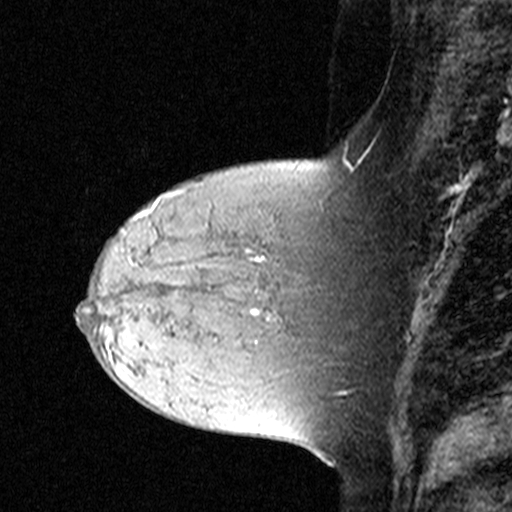
Breast MRI (dynamic contrast-enhanced), one sagittal slice. Dynamic contrast-enhanced study with each time point stored as its own series, time point 2 of 3 at this slice position (early post-contrast, ordered by acquisition time). 1.5 T. TE 4.5 ms, TR 11 ms. 3 mm slice thickness. 512 × 512 image matrix, field of view 200 × 200 mm. Female patient, age 44 years. Case-level facts recorded for this patient, not image findings: setting: breast cancer imaged before/during neoadjuvant chemotherapy; receptor status: triple-negative.
Structures marked on this image (semi-automatically segmented with operator editing):
- analysis volume of interest (the breast-tissue region the enhancement analysis was run in; not a lesion): bounding box (x1, y1, x2, y2) in pixels: (132, 212, 309, 331)
- tumour enhancement mask (voxels above the 90 % enhancement threshold inside the analysis volume of interest): (132, 212, 264, 315)